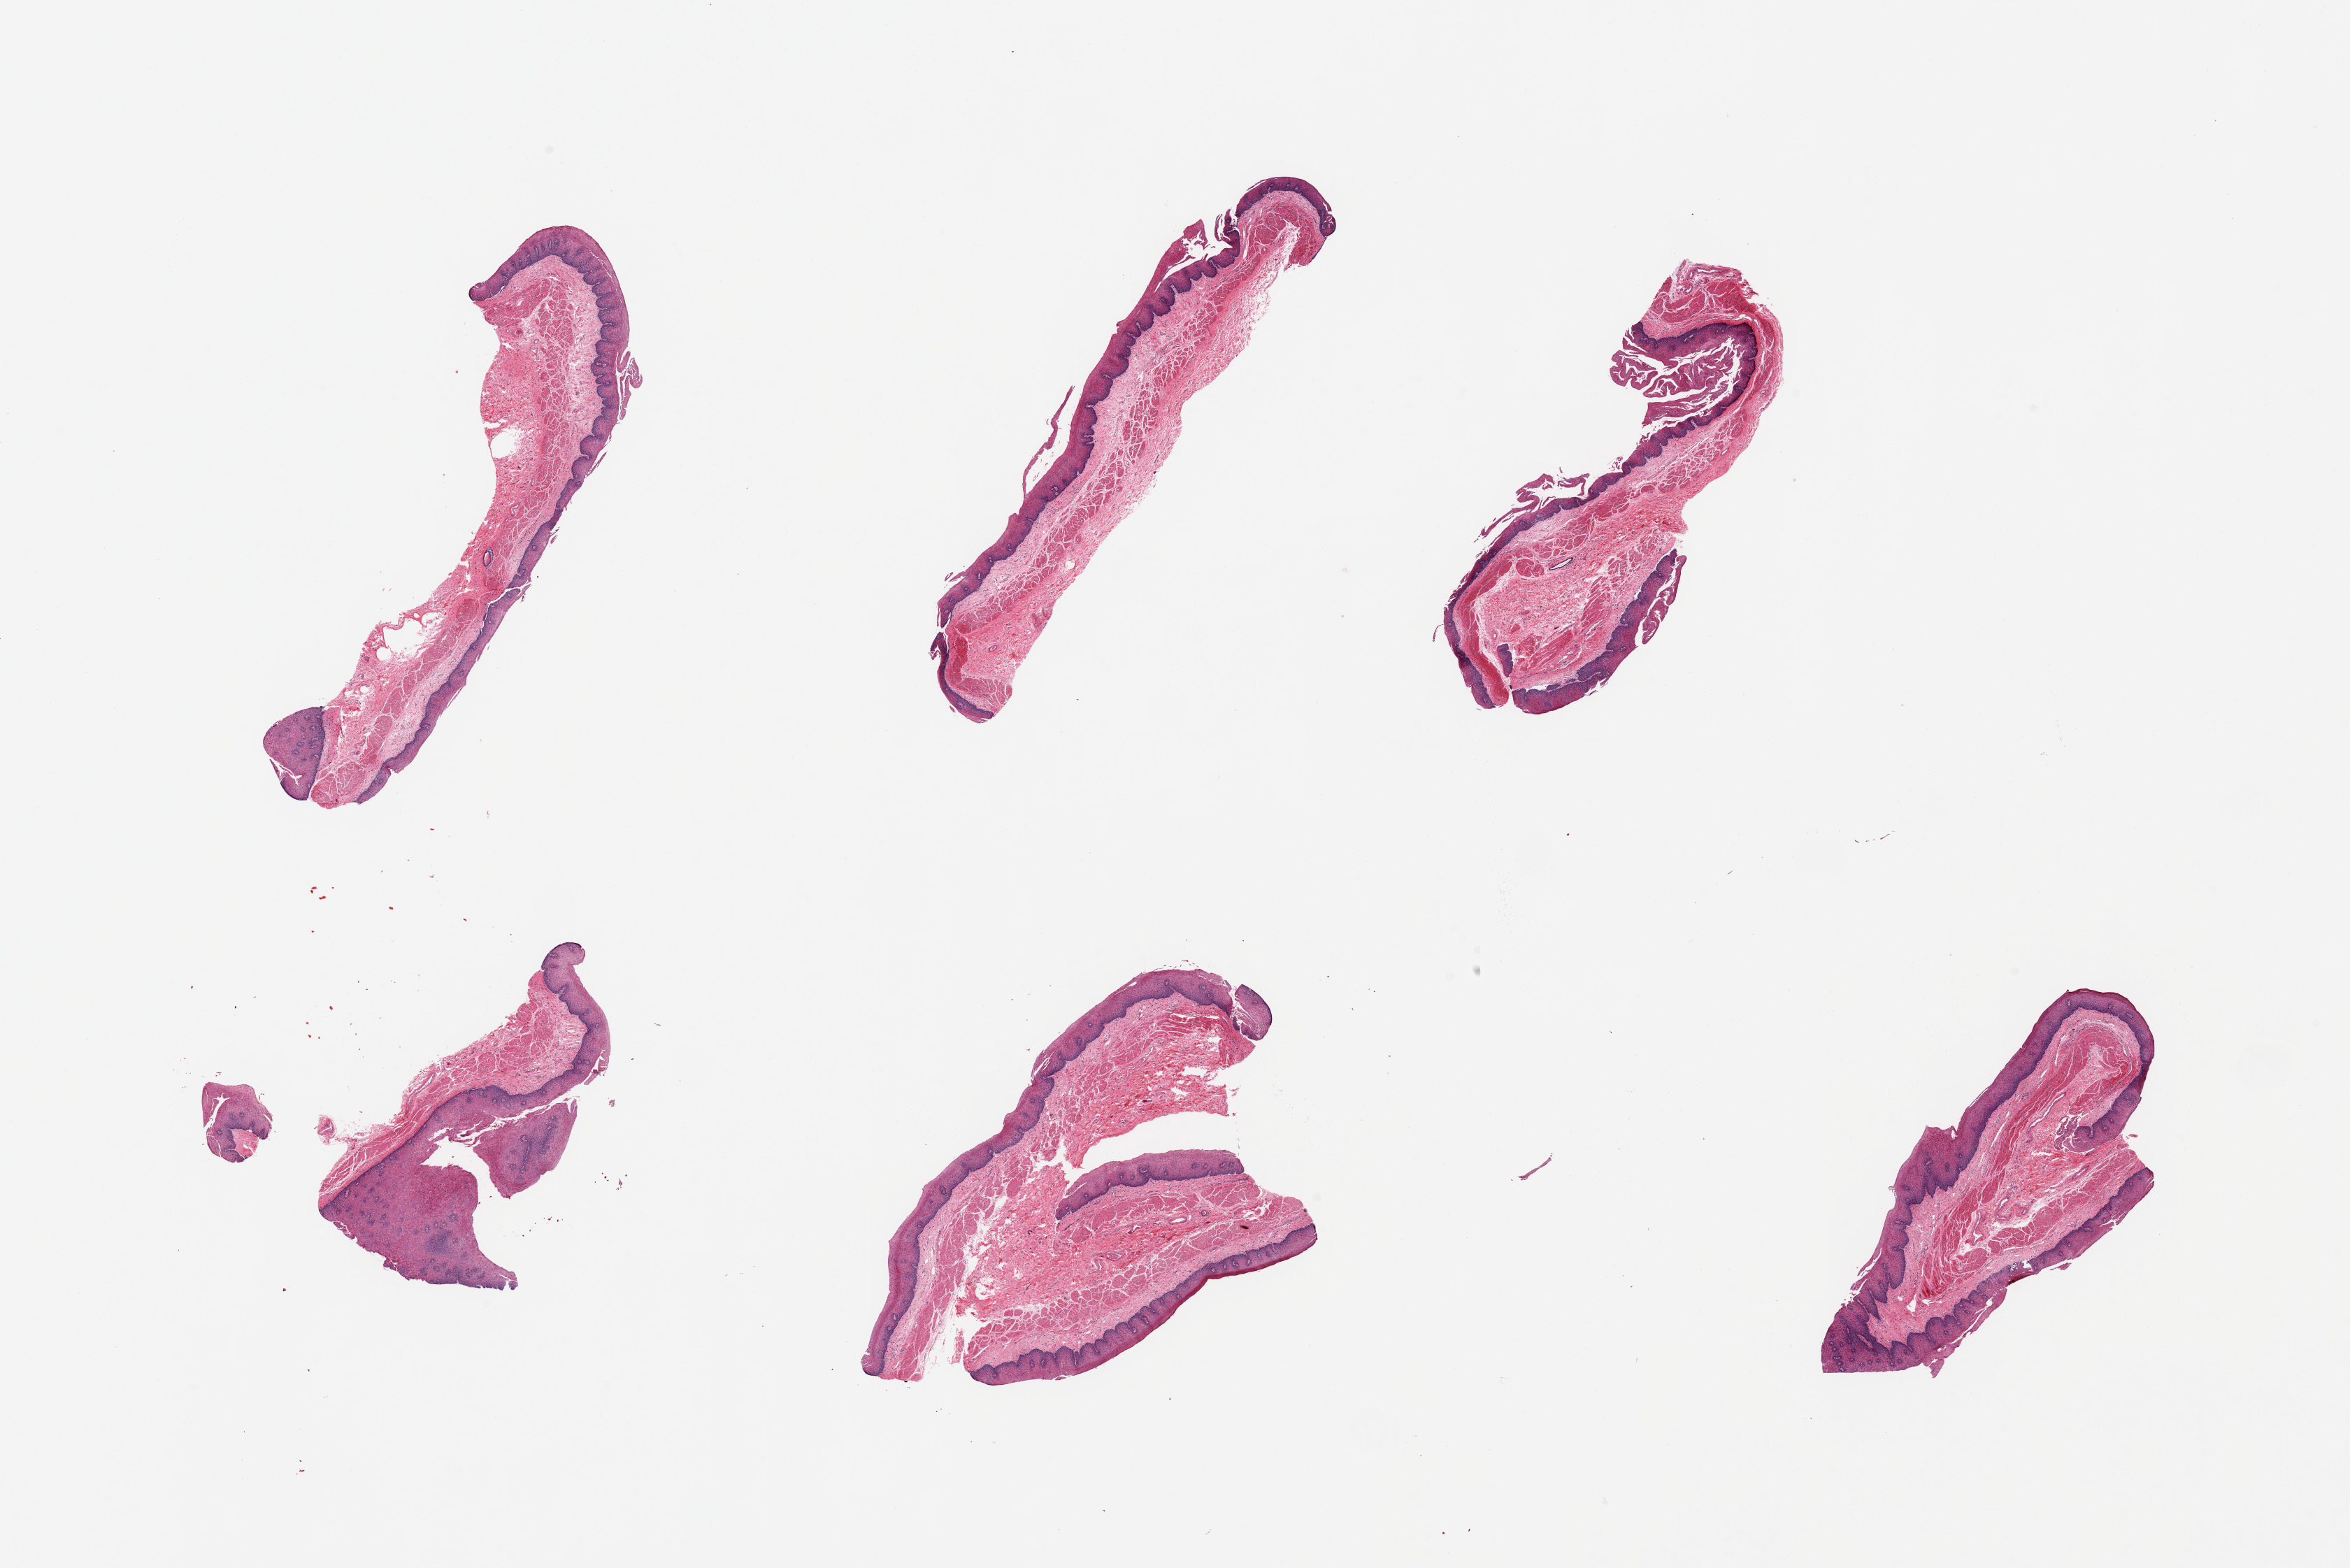
Digitized hematoxylin and eosin (H&E)-stained section, a low-resolution overview of the entire scanned area, about 26.6 x 17.7 mm (from a 20x scan). PAXgene-fixed, paraffin-embedded tissue. Target tissue: esophageal mucous membrane. Donor tissue sample. Donor sex: male.
• pathologist's review note for this sample: 6 pieces